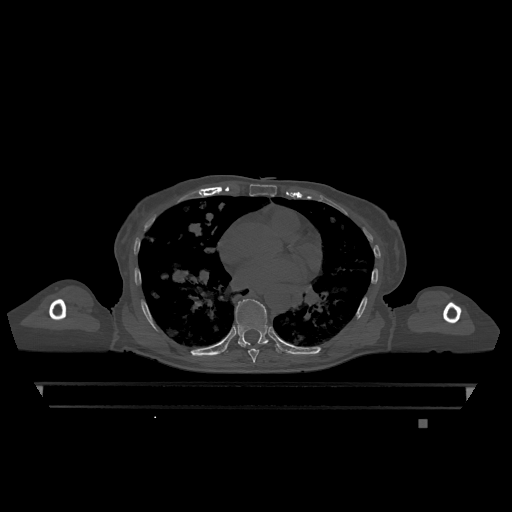
CT including the spine, one axial slice. Slice 711 of 1317 in the series (ordered by position). Bone window (W 1800 / L 400 HU). 0.5 mm slice thickness. 512 × 512 image matrix, field of view 500 × 500 mm. Patient: female, 74 years. Case-level facts recorded for this patient, not image findings: primary cancer: lung; vertebrae with lytic lesions (as recorded): T1, T4, T5, T6, L4, L5.
Annotated regions visible in this slice (semi-automatically segmented with operator editing):
- T7 vertebra: bounding box (x1, y1, x2, y2) in pixels: (242, 346, 259, 363)
- T9 vertebra: (235, 299, 282, 353)